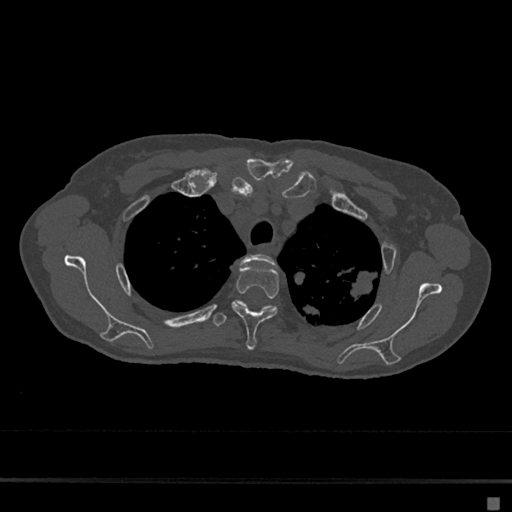
CT including the spine, one axial slice. Position 534 of 797 along the scan axis. Reconstruction kernel Br40s/3. 120 kVp. Bone window (W 1800 / L 400 HU). 0.5 mm slice thickness. 512 × 512 image matrix. Female patient, age 68 years. Case-level facts recorded for this patient, not image findings: primary cancer: renal.
Structures marked on this image (semi-automatically segmented with operator editing):
- T2 vertebra: box from (x=232, y=254) to (x=276, y=306) px
- T3 vertebra: (x=232, y=266)–(x=279, y=351)
- T4 vertebra: (x=212, y=305)–(x=275, y=327)